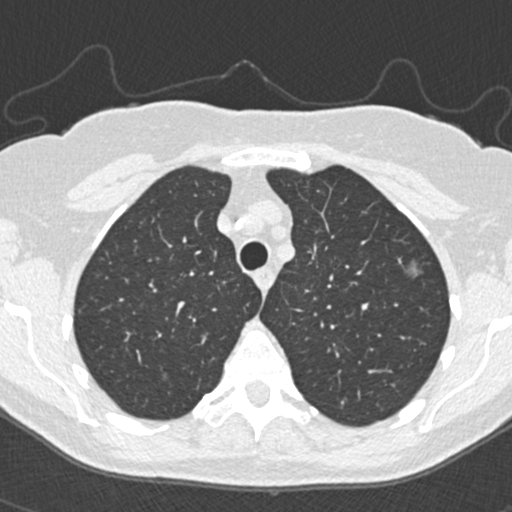
Low-dose screening chest CT, one axial slice. Position 283 of 350 along the scan axis. Reconstruction kernel B30f. Lung window (W 1500 / L -600 HU). 1 mm slice thickness. 512 × 512 image matrix.
Annotated regions visible in this slice (manually delineated by an expert):
- lesion 3 (tumor, upper lobe of left lung): bounding box [x1, y1, x2, y2] px = [408, 264, 419, 278]